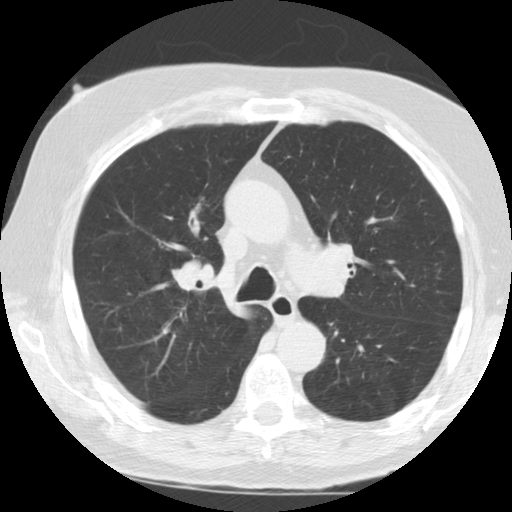
Axial slice from a low-dose chest CT screening exam, second annual screen, lung window (W 1500 / L -600 HU), standard (soft-tissue) reconstruction kernel (STANDARD), 512 × 512 image matrix. Male participant, aged 72 years at enrolment.
Expert-annotated lung lesion, box from (x=157, y=238) to (x=226, y=310) px. Screening reader's record for this exam: no non-calcified nodule ≥4 mm recorded. Official screen result: negative screen, minor abnormalities not suspicious for lung cancer. Participant outcome: lung cancer diagnosed 415 days after this screen (after the third annual screen) — small cell carcinoma, NOS, right upper lobe, stage IV (AJCC 6th edition), 7 mm at pathology.